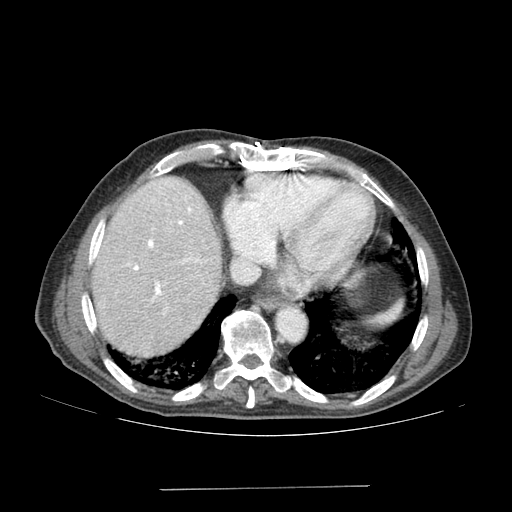
Contrast-enhanced abdominal CT (liver protocol), one axial slice; slice 148 of 192 in the series (ordered by position); reconstruction kernel SOFT; 120 kVp; soft-tissue window (W 400 / L 40 HU); 2.5 mm slice thickness; 512 × 512 image matrix, field of view 400 × 400 mm. From the clinical record (not read from this slice): diagnosis: hepatocellular carcinoma (patient treated with transarterial chemoembolisation; whether this scan precedes or follows treatment is not stated here); TNM stage (as recorded): Stage-IVA.
Outlined on this slice (semi-automatic segmentation, software-assisted and operator-edited):
- liver parenchyma outside the tumour (the mass and vessels are separate outlines, so this box may not span the whole liver): box from (x=92, y=176) to (x=220, y=356) px
- liver vessels: (x=134, y=207)–(x=199, y=299)